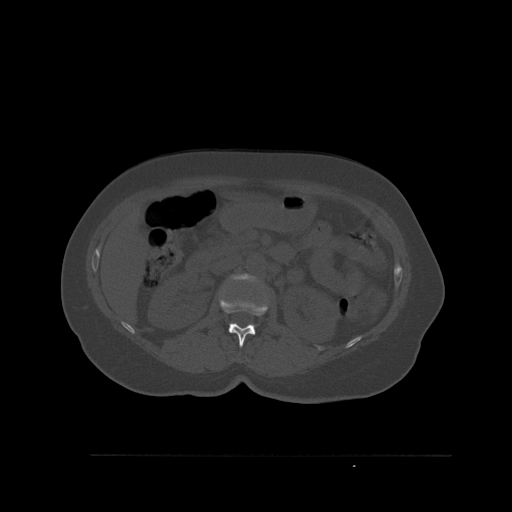
CT including the spine, one axial slice. Slice 261 of 527 in the series (ordered by position). Bone window (W 1800 / L 400 HU). 1.5 mm slice thickness. 512 × 512 image matrix, field of view 470 × 470 mm. Female patient, age 73 years. Case-level facts recorded for this patient, not image findings: primary cancer: breast; vertebrae with lytic lesions (as recorded): L2.
Outlined on this slice (semi-automatic segmentation, software-assisted and operator-edited):
- L1 vertebra: bounding box <219,297,268,347> (left, top, right, bottom; pixels)
- L2 vertebra: <232,273,257,282>